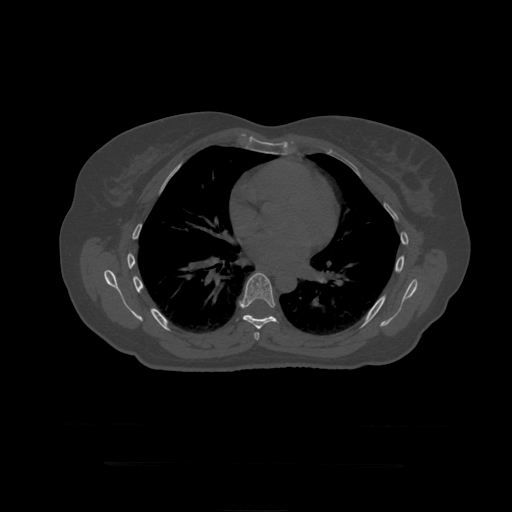
CT including the spine, one axial slice. Slice 281 of 399 in the series (ordered by position). Bone window (W 1800 / L 400 HU). 1.25 mm slice thickness. 512 × 512 image matrix. Patient age 41 years. From the clinical record (not read from this slice): primary cancer: breast.
Outlined on this slice (semi-automatic segmentation, software-assisted and operator-edited):
- T7 vertebra: bounding box <254,332,260,341> (left, top, right, bottom; pixels)
- T8 vertebra: <240,273,279,330>
- T9 vertebra: <245,315,251,316>